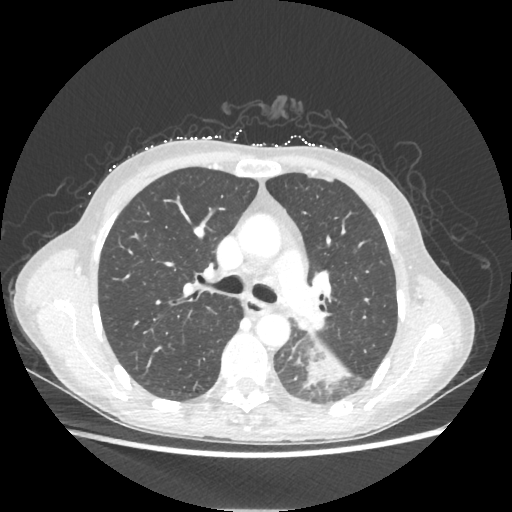
Chest CT, one axial slice. Slice 136 of 221 in the series (ordered by position). 80 kVp. Lung window (W 1500 / L -600 HU). 1.25 mm slice thickness. 512 × 512 image matrix, field of view 360 × 360 mm. Female patient, age 53 years. Case-level facts recorded for this patient, not image findings: clinical TNM (as recorded): T3 N0 M0.
Outlined on this slice (rectangle marked by the reading radiologist):
- lung tumour (recorded histology: adenocarcinoma): bounding box (x1, y1, x2, y2) in pixels: (304, 343, 351, 389)